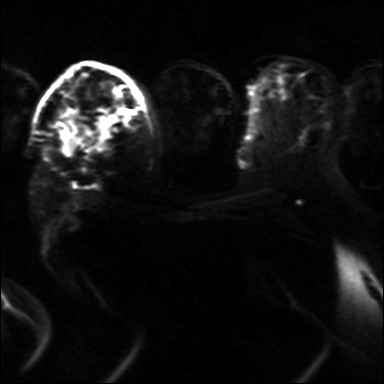
Breast MRI, one axial slice. Slice 22 of 36 in the series (ordered by position). Diffusion-weighted series; image 2 of 4 stored at this slice position (different b-values; order by instance number). 3 T. 384 × 384 image matrix. Female patient.
Structures marked on this image (expert manual segmentation):
- tumour on diffusion-weighted imaging: bounding box [x1, y1, x2, y2] px = [61, 109, 119, 156]